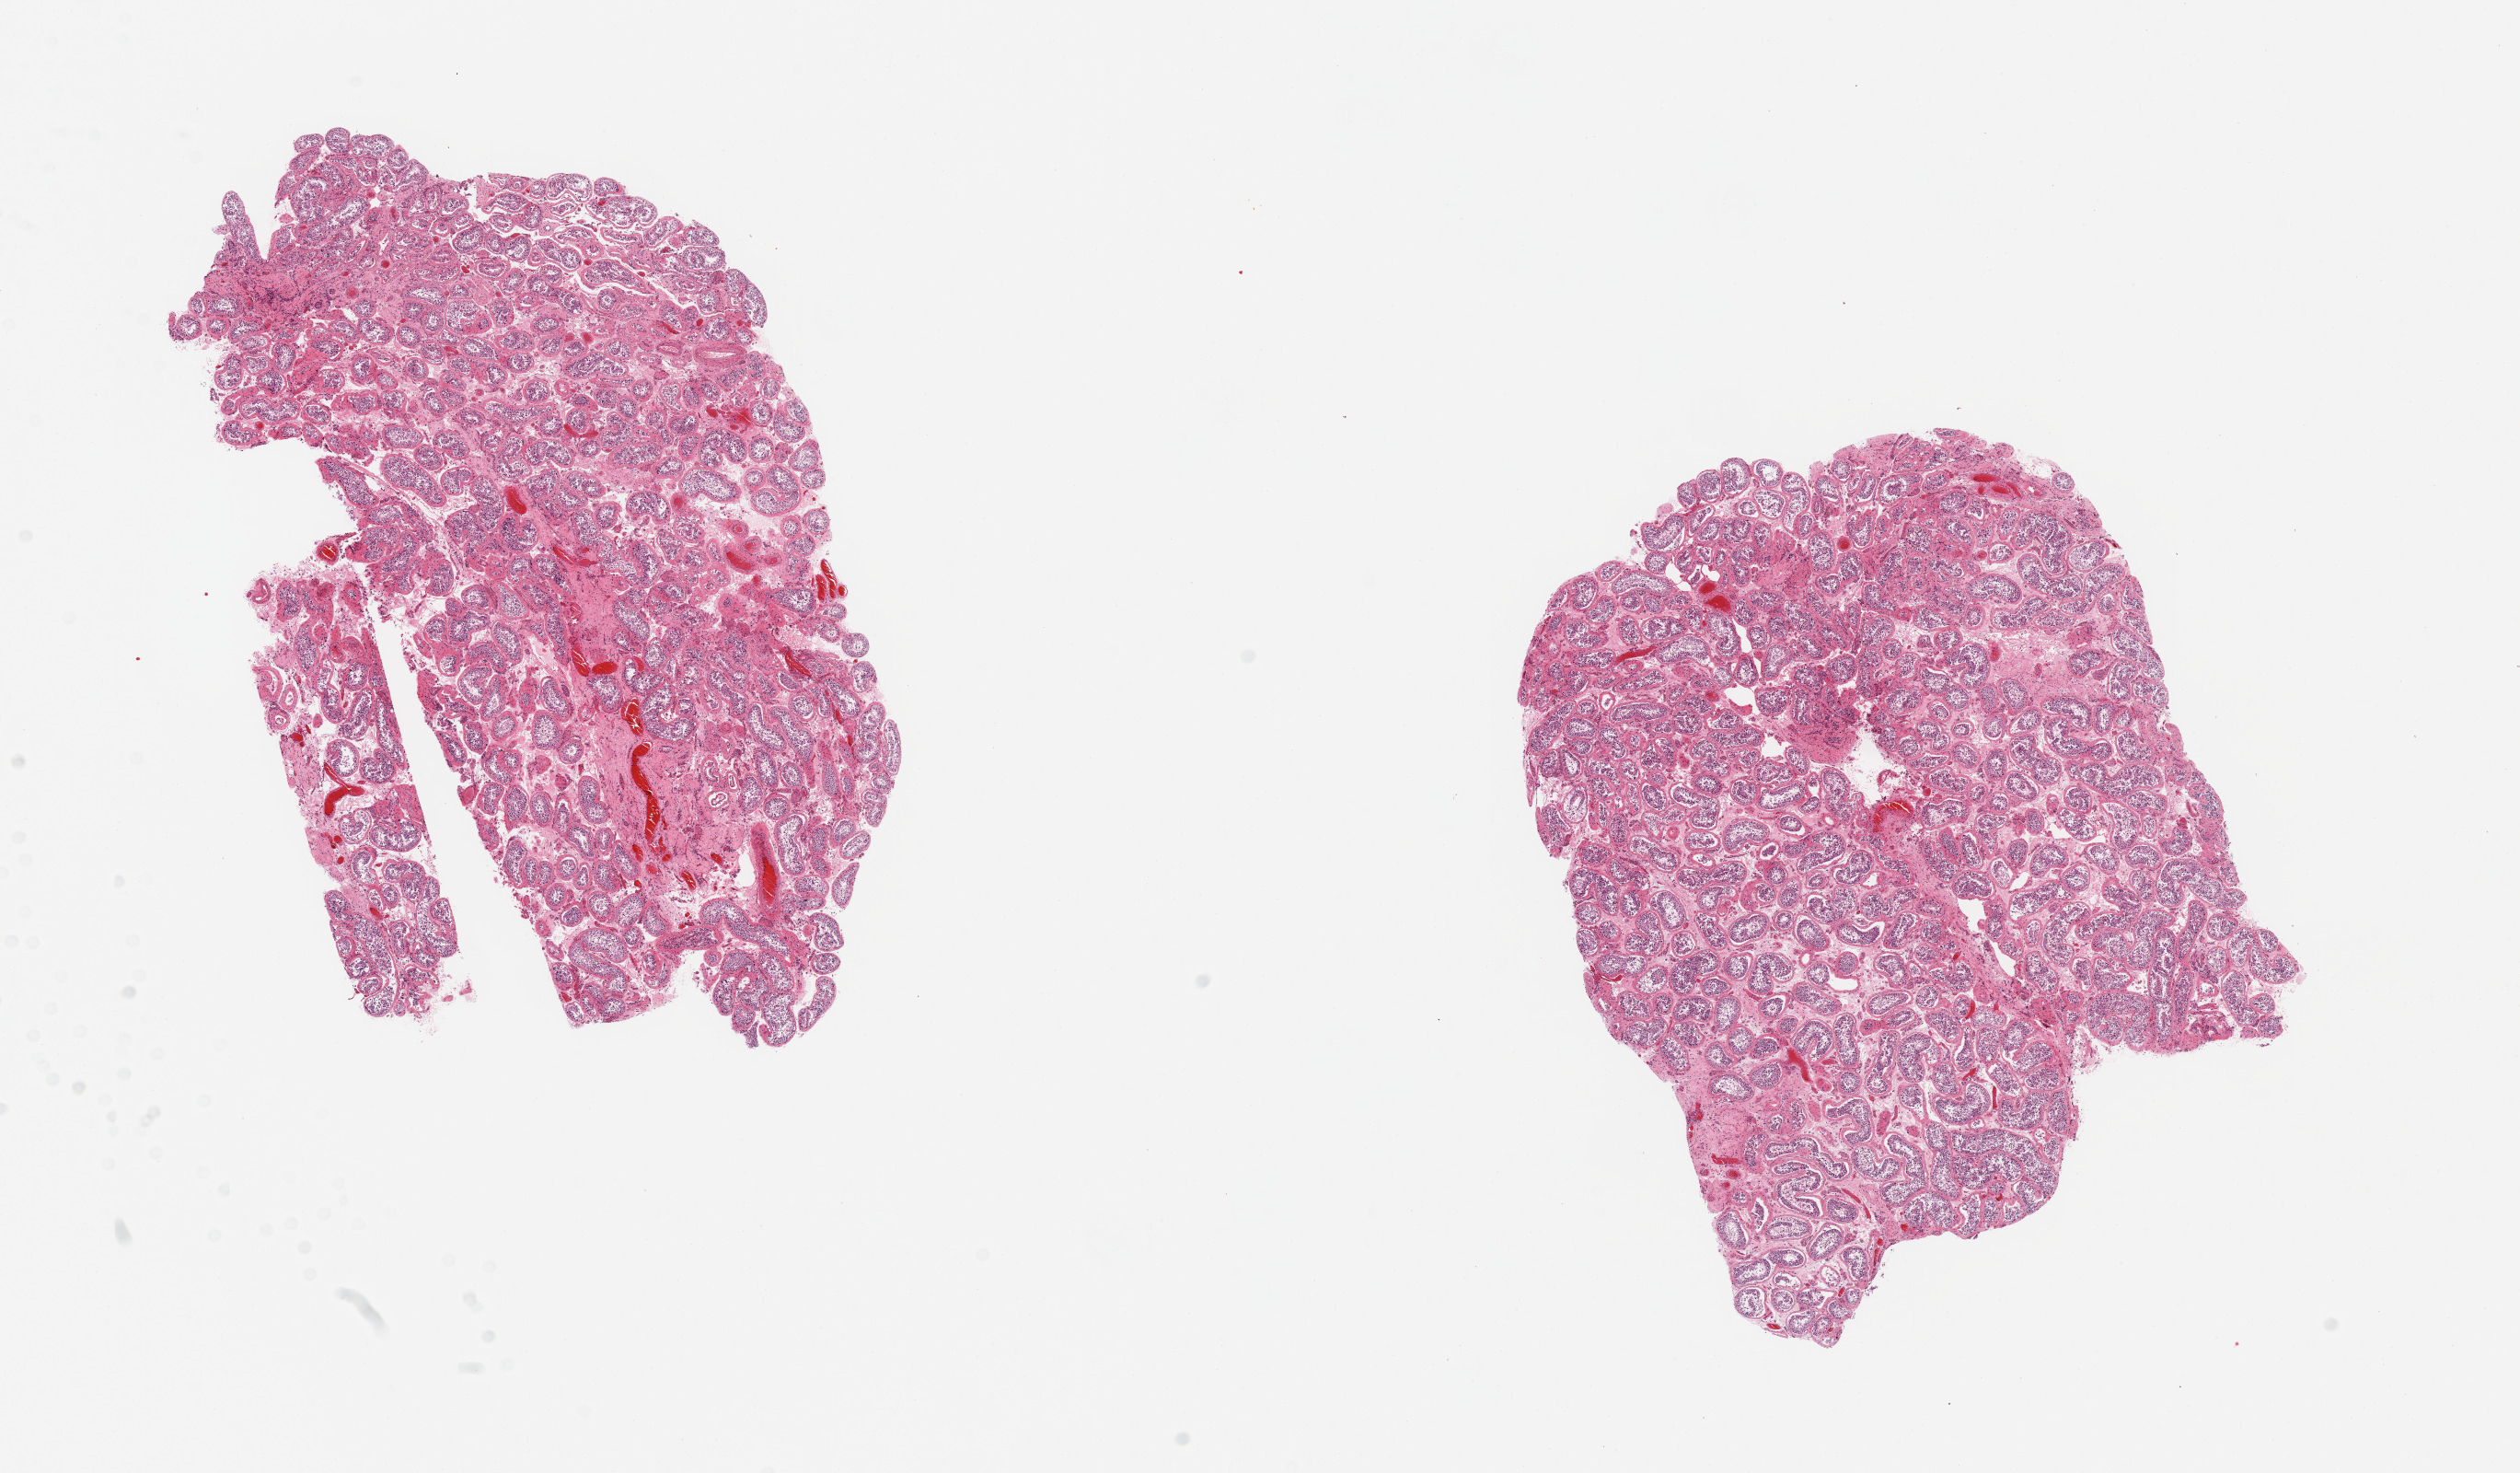
Hematoxylin and eosin (H&E) whole-slide image, brightfield, a low-resolution overview of the entire scanned area, about 21.7 x 12.7 mm; PAXgene-fixed, paraffin-embedded tissue; target tissue: testis; donor tissue sample. Male donor.
Review note (as recorded): 2 pieces; spermatogenesis present; few hyalinized tubules.